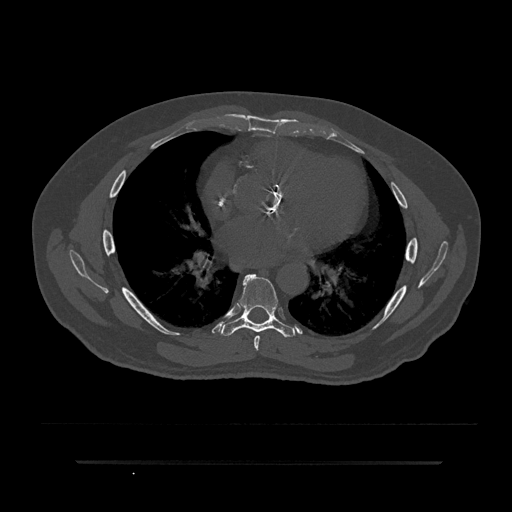
CT including the spine, one axial slice; slice 487 of 797 in the series (ordered by position); reconstruction kernel Br40s/3; bone window (W 1800 / L 400 HU); 0.5 mm slice thickness; 512 × 512 image matrix, field of view 464 × 464 mm. Male patient, age 59 years. Case-level facts recorded for this patient, not image findings: primary cancer: bile ducts; vertebrae with lytic lesions (as recorded): T10.
Structures marked on this image (semi-automatic segmentation, software-assisted and operator-edited):
- T6 vertebra: box from (x=254, y=336) to (x=260, y=351) px
- T7 vertebra: (x=221, y=274)–(x=295, y=338)